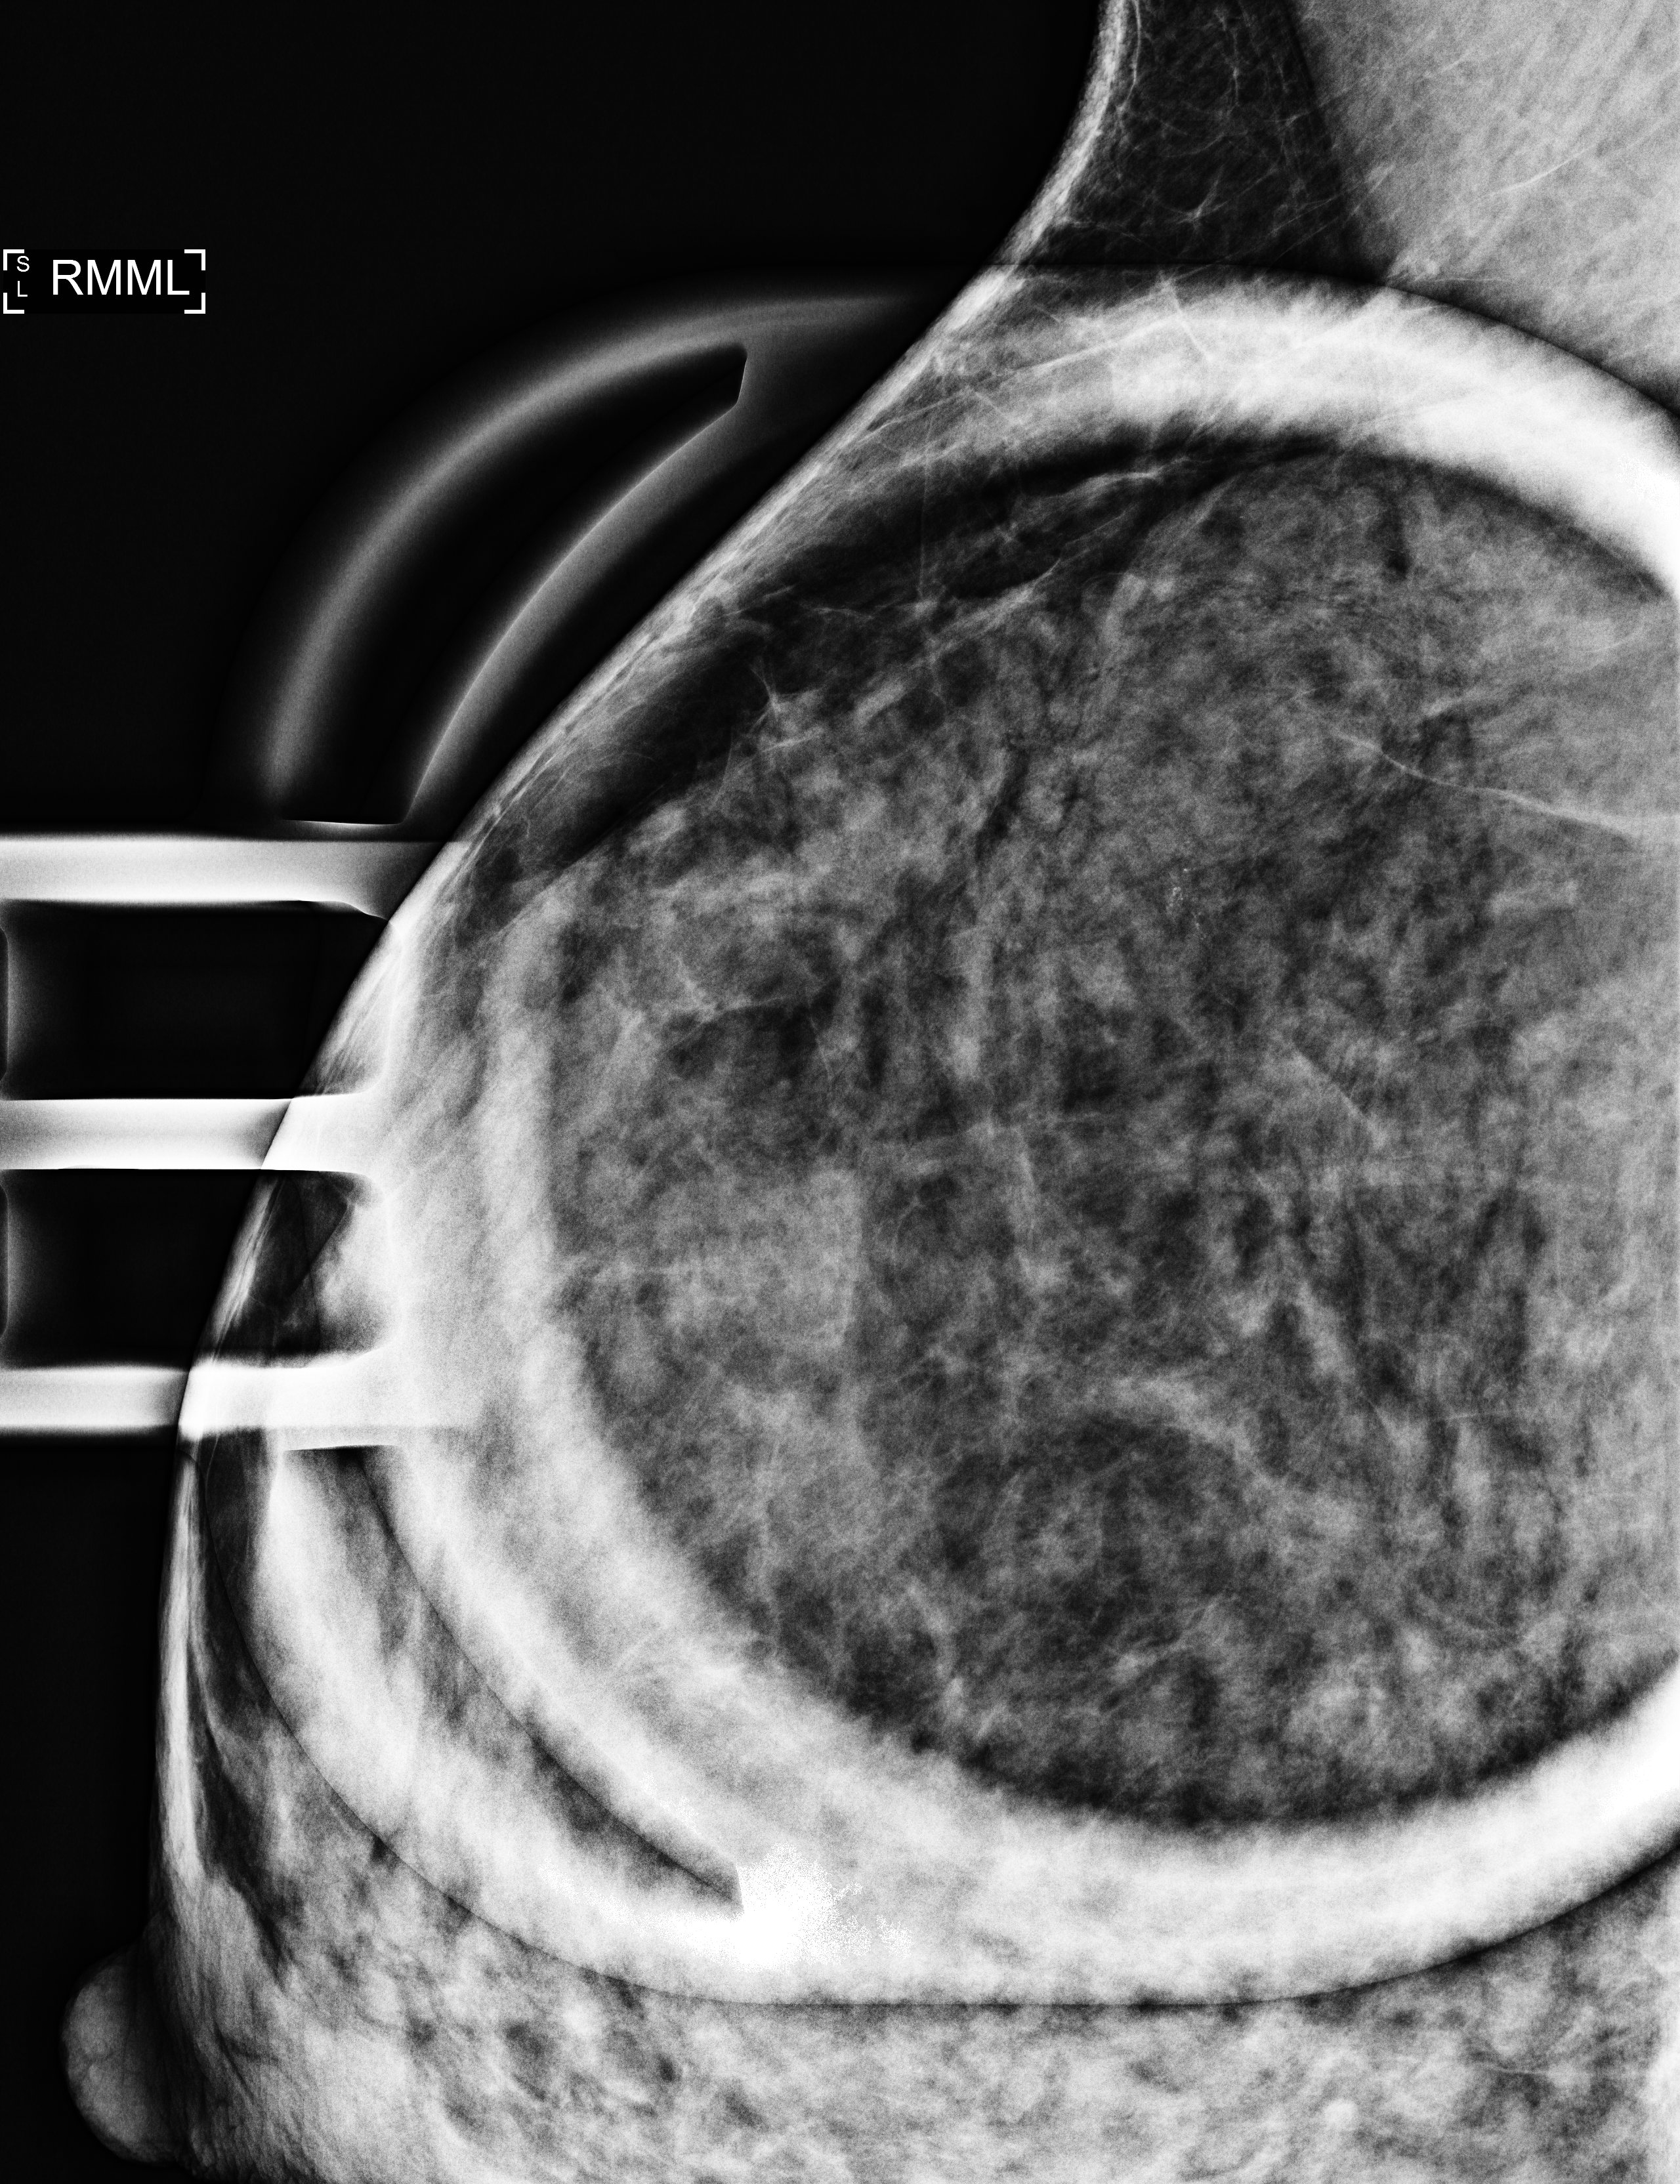
Additional (diagnostic) view. Patient aged 45 years (female).
Image type: full-field digital mammogram. Breast: right. Projection: ML view, magnification.